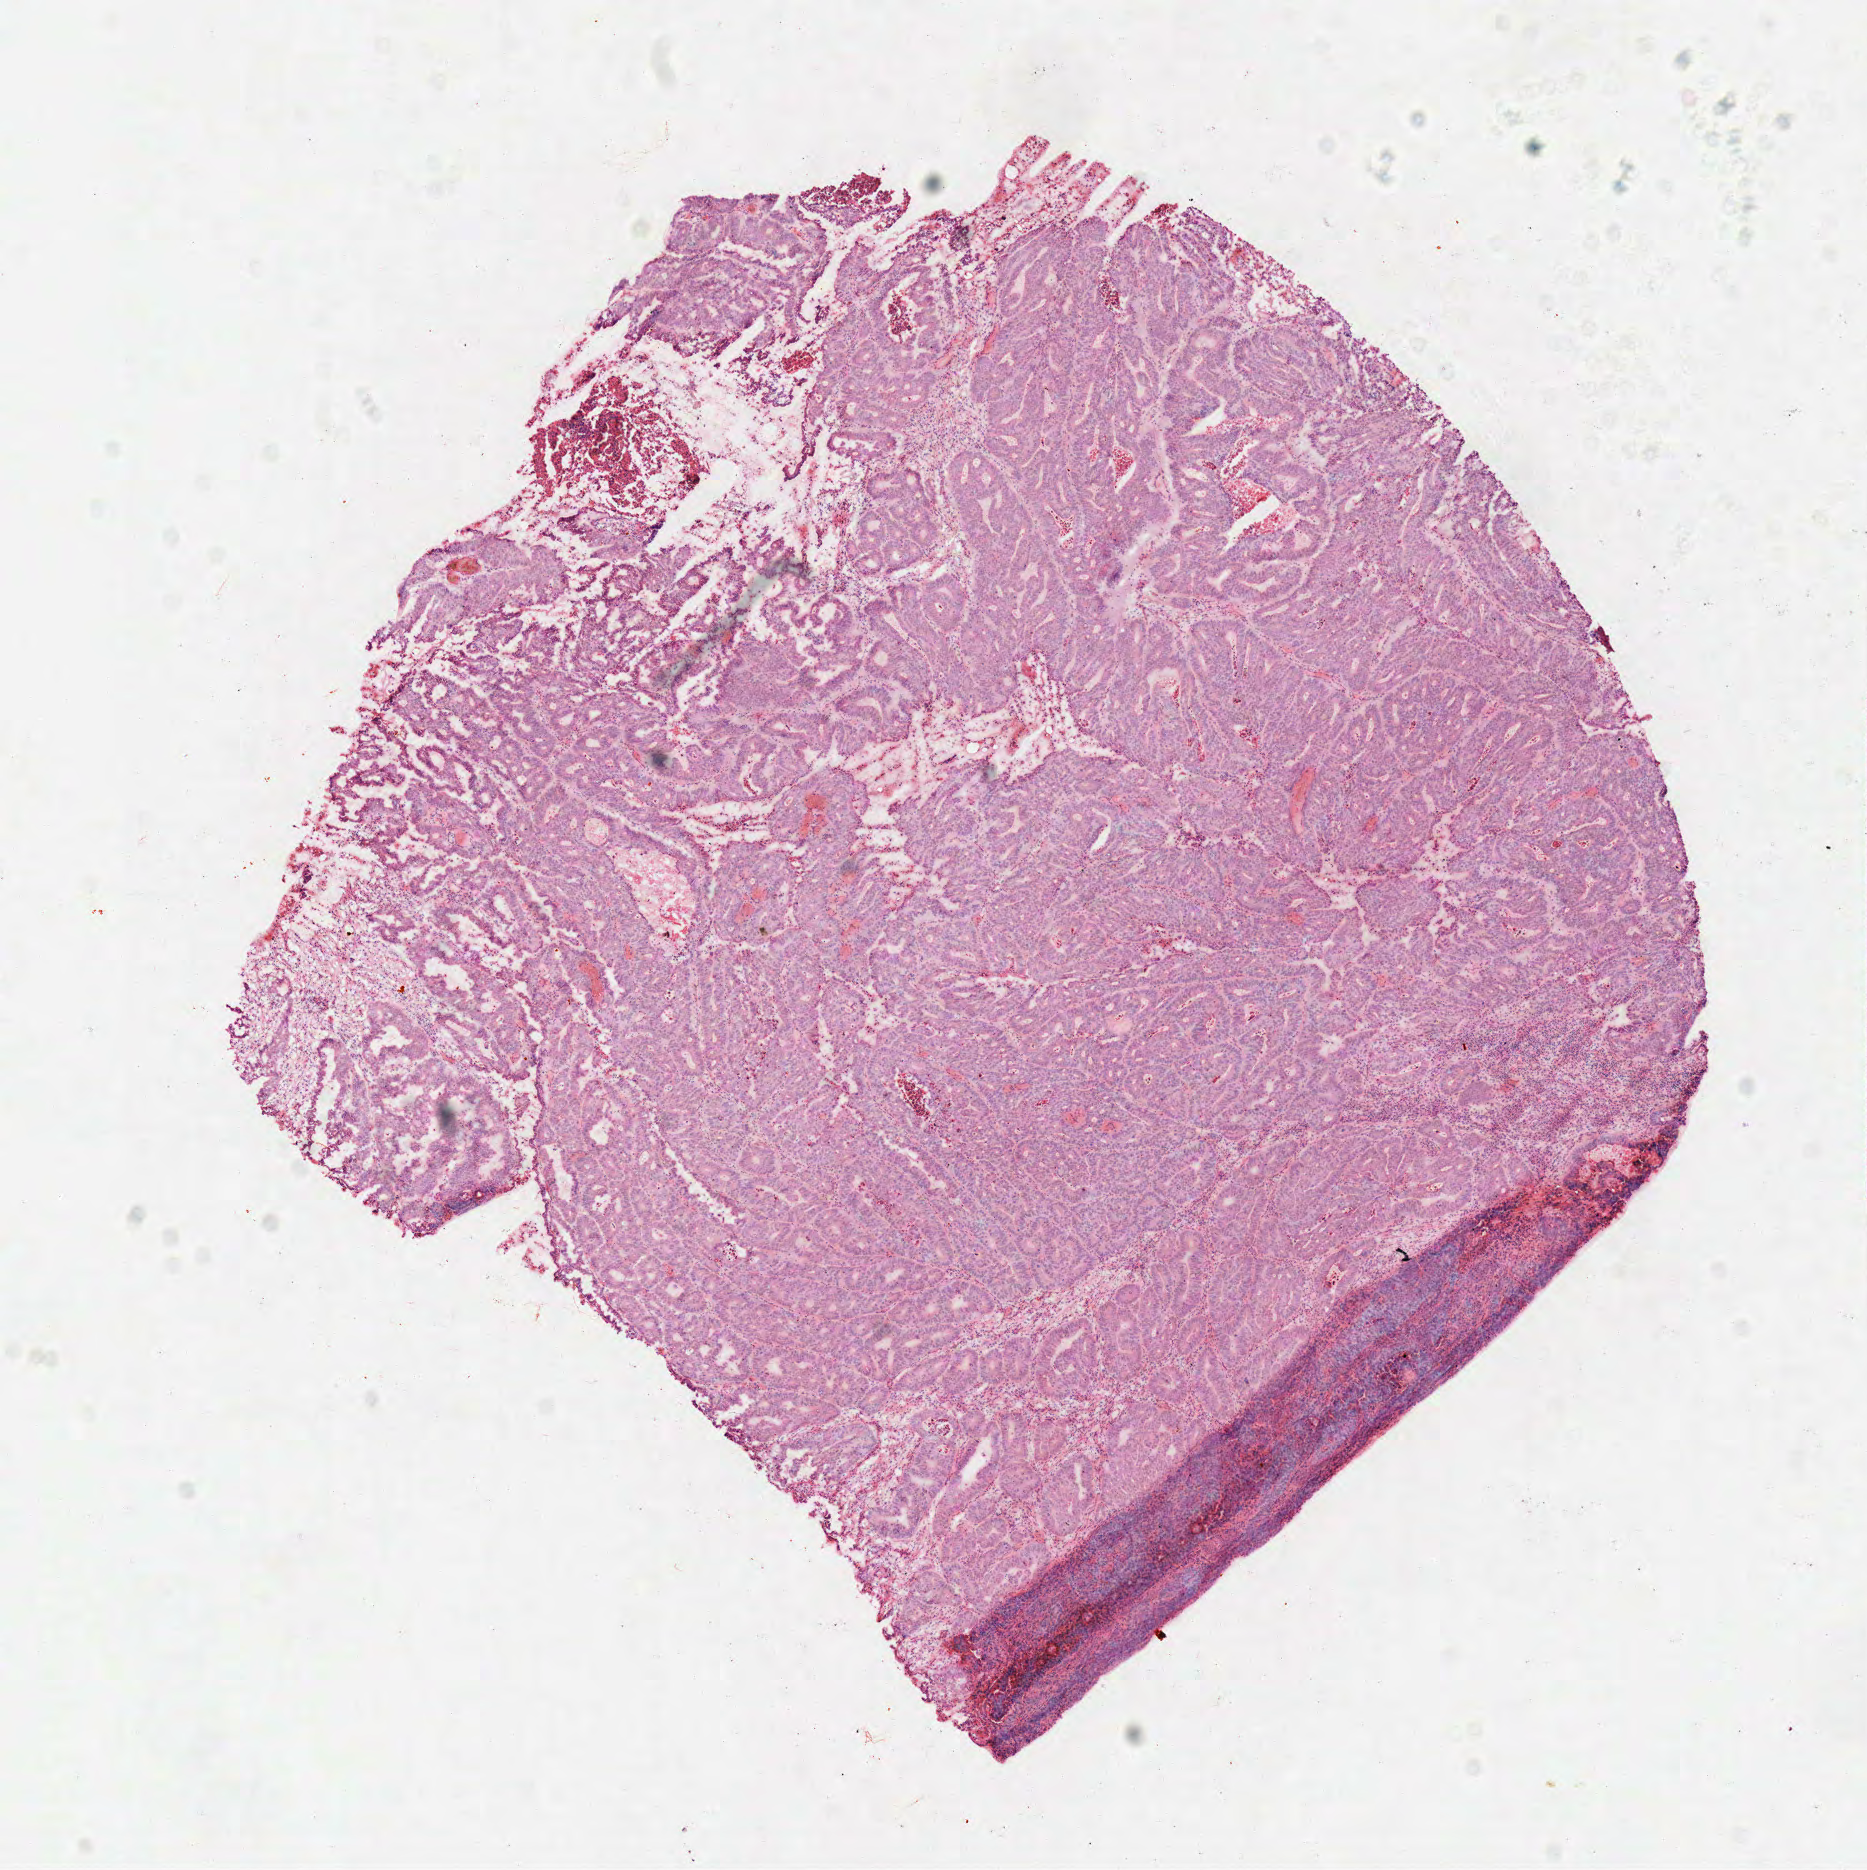
Digitized H&E tissue section (whole slide) — whole scanned area (about 7.3 x 7.4 mm, slide scanned at 40x) shown as a low-resolution overview, frozen section from the top of the tissue portion, sample: primary tumour, colon. Male patient; age at initial diagnosis 61 years. Composition of this section per pathologist review: tumour cells 97%, tumour nuclei 80%, normal cells 0%, stromal cells 0%, necrosis 3%. Inflammatory infiltration, as recorded: lymphocyte infiltration 5%, monocyte infiltration 0%, neutrophil infiltration 0%.
AJCC pathologic stage: IIA. Pathologic diagnosis: Adenocarcinoma, NOS.